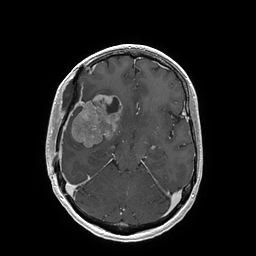
Brain MRI from a brain-tumour surgery series, one axial slice. Position 103 of 202 along the scan axis. T1-weighted post-contrast. 1 mm slice thickness. 256 × 256 image matrix, field of view 250 × 250 mm. From the clinical record (not read from this slice): histopathology: Glioblastoma; WHO grade: 4; IDH mutation: no.
Annotated regions visible in this slice (manually delineated by an expert):
- tumour: bounding box (x1, y1, x2, y2) in pixels: (71, 95, 121, 148)